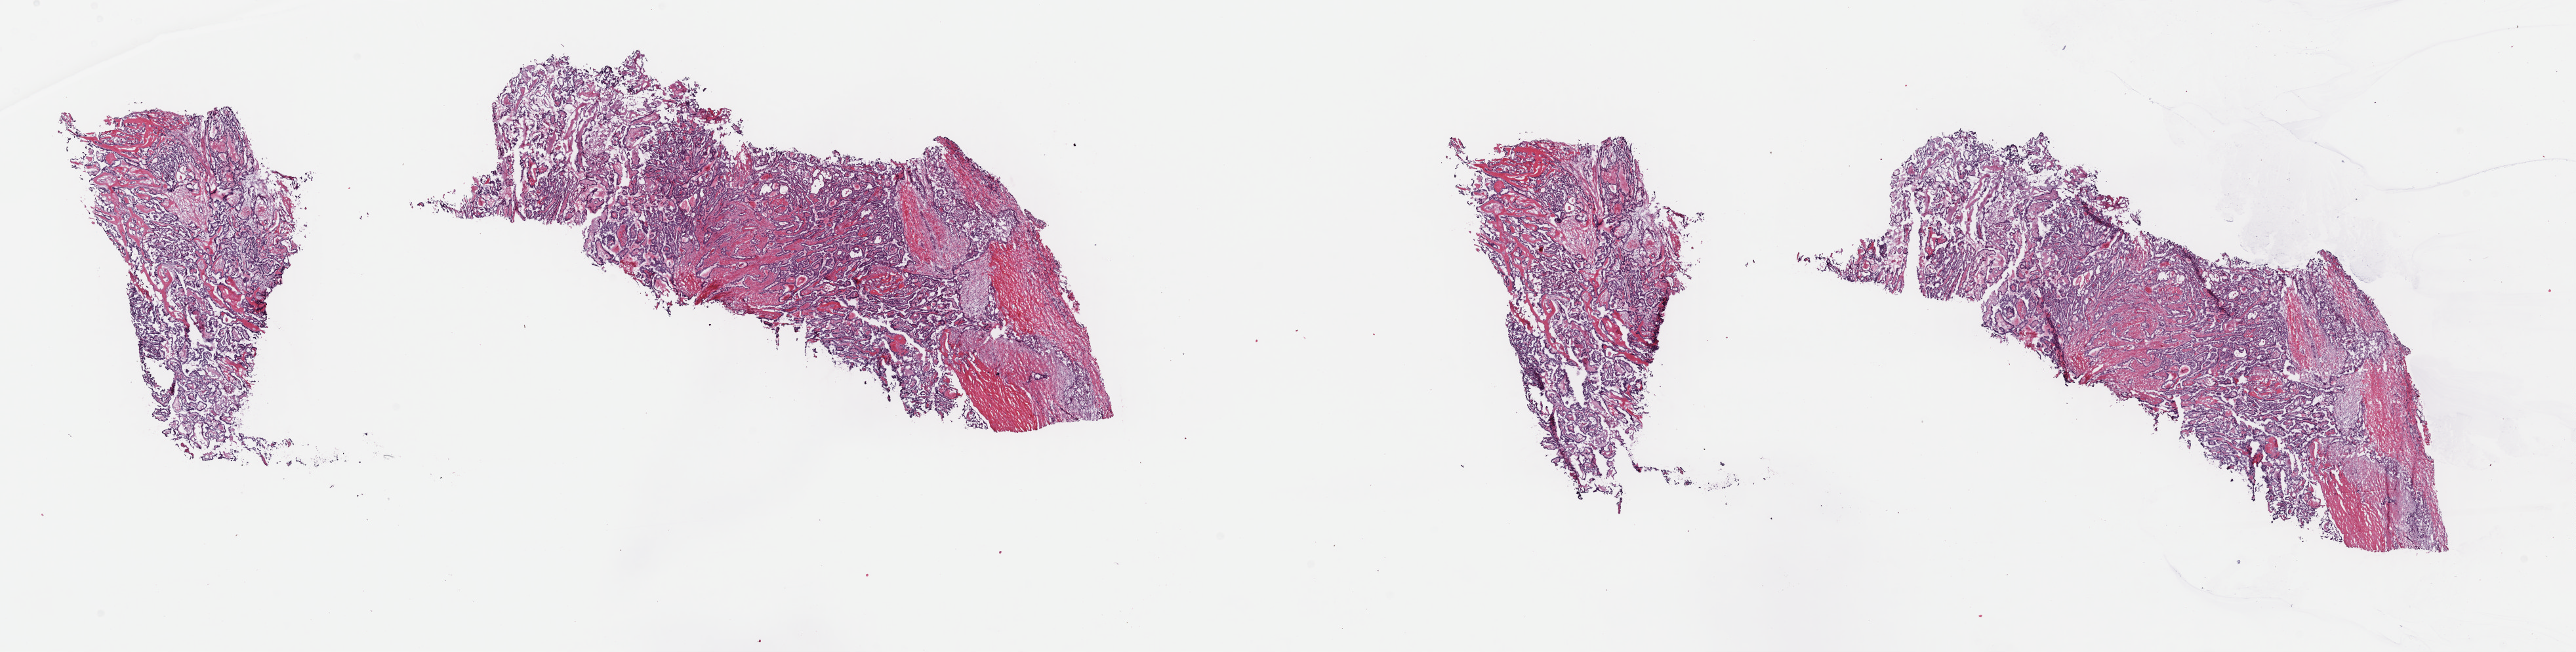
Digitized Hematoxylin and eosin (H&E) stained tissue section (whole slide) — shown as a low-resolution overview of the whole scanned area (about 31.0 x 7.8 mm, from a 40x scan). Frozen section. Thyroid, primary tumour sample. Female patient; age at initial diagnosis 61 years. Pathologist review of this section (percent, as recorded): tumour cells 95%, tumour nuclei 80%, normal cells 0%, stromal cells 5%, necrosis 0%. Inflammatory infiltration, as recorded: lymphocyte infiltration 0%, monocyte infiltration 0%, neutrophil infiltration 0%.
- pathologic diagnosis: Papillary adenocarcinoma, NOS
- AJCC pathologic stage: III (6th edition)
- TNM: T3 N0 M0